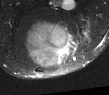
MRI of an extremity soft-tissue mass, one axial slice. T2-weighted fat-saturated. MR volume resampled by the dataset authors to the PET/CT grid (not the native acquisition matrix). 109 × 95 image matrix, field of view 106 × 93 mm. Male patient. Case-level facts recorded for this patient, not image findings: histological type: synovial sarcoma; site of the primary tumour: left poplietal fossa.
Outlined on this slice (expert contour drawn on MRI and transferred to this co-registered scan by the dataset authors):
- gross tumour volume (mass): bounding box (x1, y1, x2, y2) in pixels: (26, 22, 71, 66)